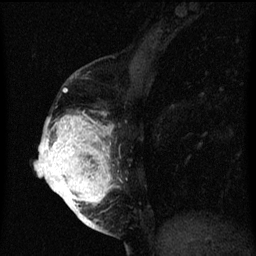
Breast MRI (dynamic contrast-enhanced), one sagittal slice. Position 24 of 60 along the scan axis. Dynamic contrast-enhanced series, image 2 of 3 at this slice position (ordered by acquisition). 1.5 T. TE 4.2 ms, TR 8 ms. 256 × 256 image matrix. Female patient, age 56 years.
Outlined on this slice (semi-automatically segmented with operator editing):
- analysis volume of interest (the breast-tissue region the enhancement analysis was run in; not a lesion): bounding box <40,112,121,219> (left, top, right, bottom; pixels)
- tumour enhancement mask (voxels above the 70 % enhancement threshold inside the analysis volume of interest): <40,114,113,219>